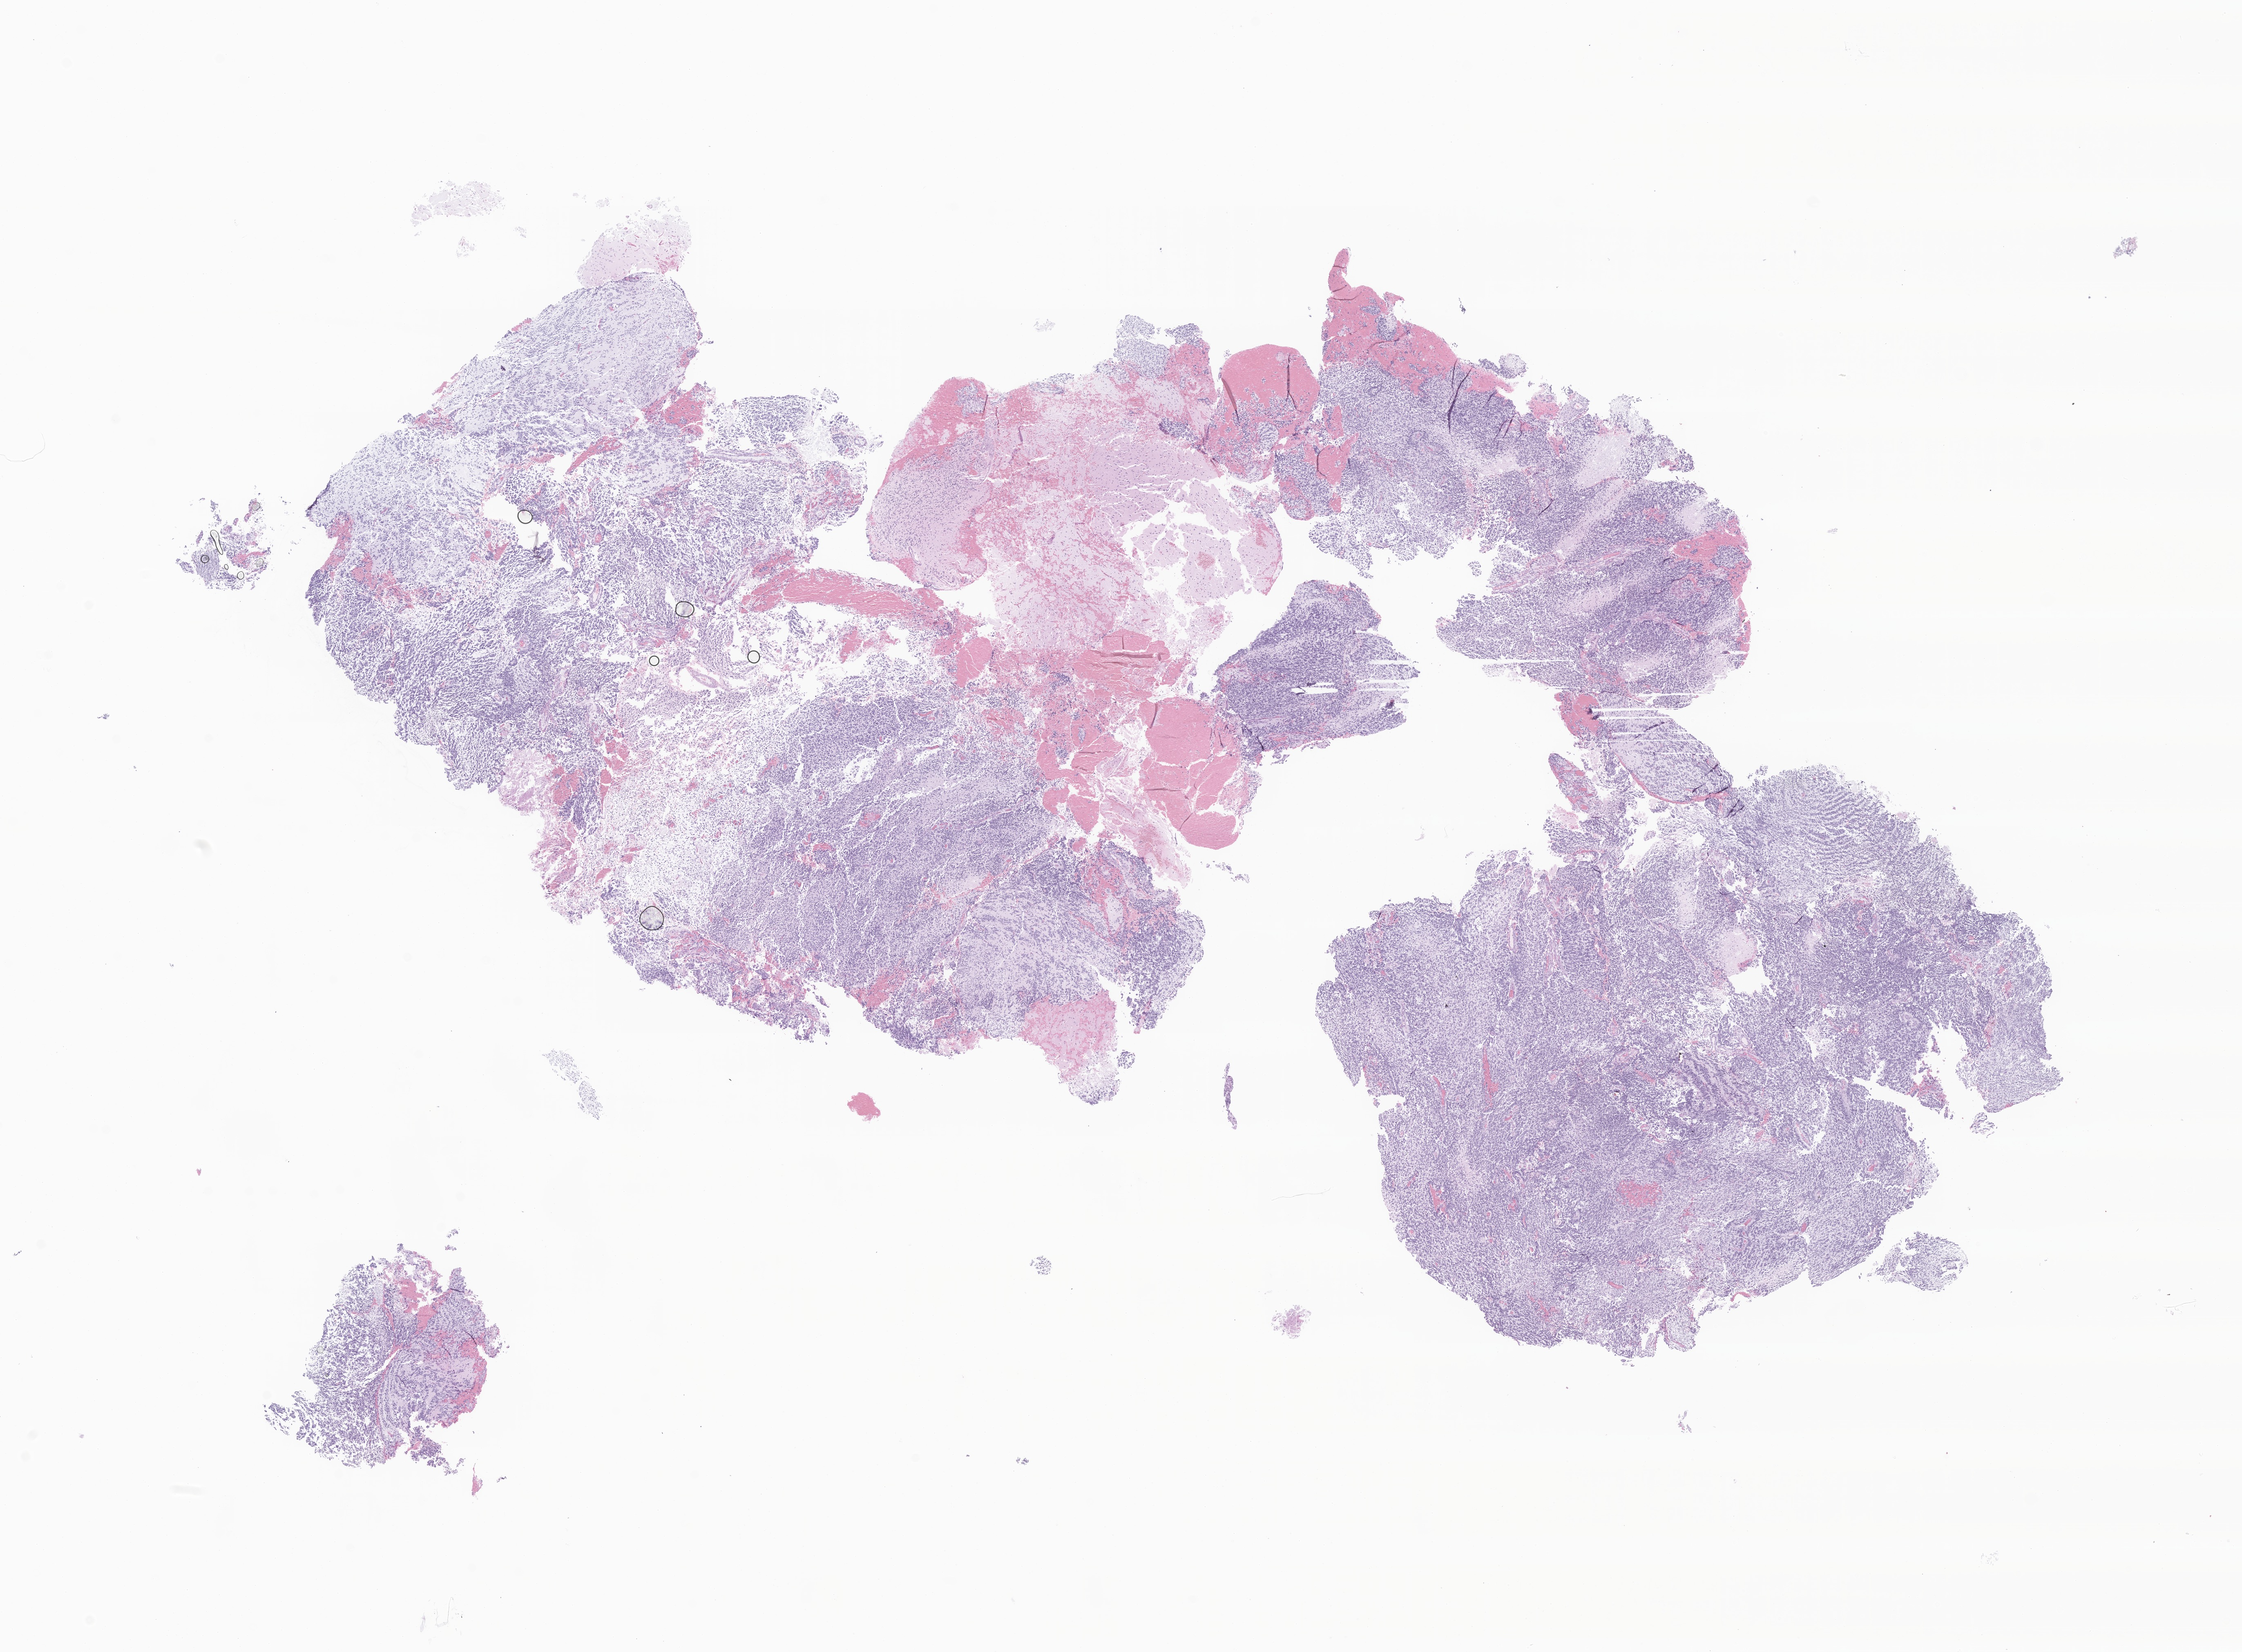
Hematoxylin and eosin (H&E) whole-slide image of tumor tissue from the brain — whole scanned area (about 23.1 x 17.0 mm) shown as a low-resolution overview. Formalin-fixed, paraffin-embedded (FFPE) tissue. Patient female; age 146 months.
Diagnosis (ICD-O-3 morphology term): Glioma, malignant.